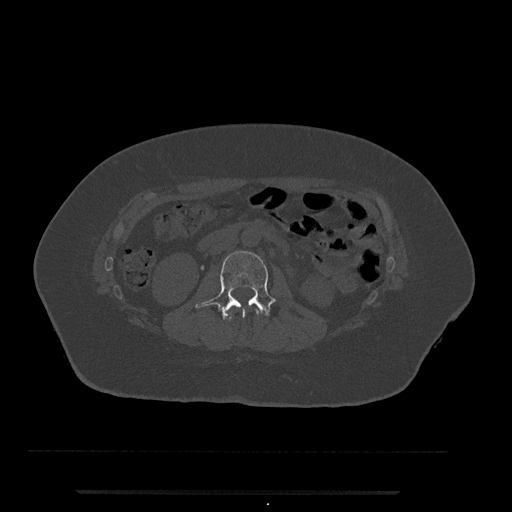
CT including the spine, one axial slice. Position 41 of 797 along the scan axis. Bone window (W 1800 / L 400 HU). 0.5 mm slice thickness. 512 × 512 image matrix, field of view 440 × 440 mm. Patient: female, 51 years. Case-level facts recorded for this patient, not image findings: primary cancer: neuro; vertebrae with lytic lesions (as recorded): T8.
Outlined on this slice (semi-automatically segmented with operator editing):
- L1 vertebra: bounding box [x1, y1, x2, y2] px = [227, 309, 262, 321]
- L2 vertebra: [195, 251, 277, 321]